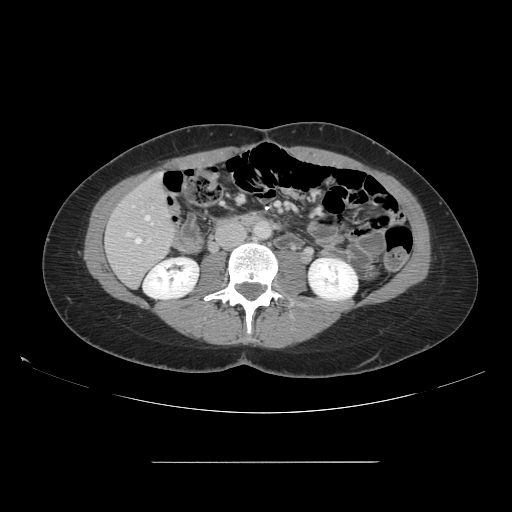
Contrast-enhanced abdominal CT, one axial slice. Slice 45 of 151 in the series (ordered by position). Intravenous contrast given. Soft-tissue window (W 400 / L 40 HU). 2.5 mm slice thickness. 512 × 512 image matrix, field of view 421 × 421 mm. Female patient, age 46 years. Case-level facts recorded for this patient, not image findings: diagnosis: colorectal cancer liver metastases, imaged before liver resection; multiple liver metastases: yes; largest metastasis: 3 cm; chemotherapy before resection: no.
Outlined on this slice (outlined manually by an expert reader):
- hepatic veins: bounding box [x1, y1, x2, y2] px = [136, 216, 150, 243]
- liver: [106, 176, 176, 286]
- planned liver remnant (the part of the liver to remain after resection): [106, 176, 175, 287]